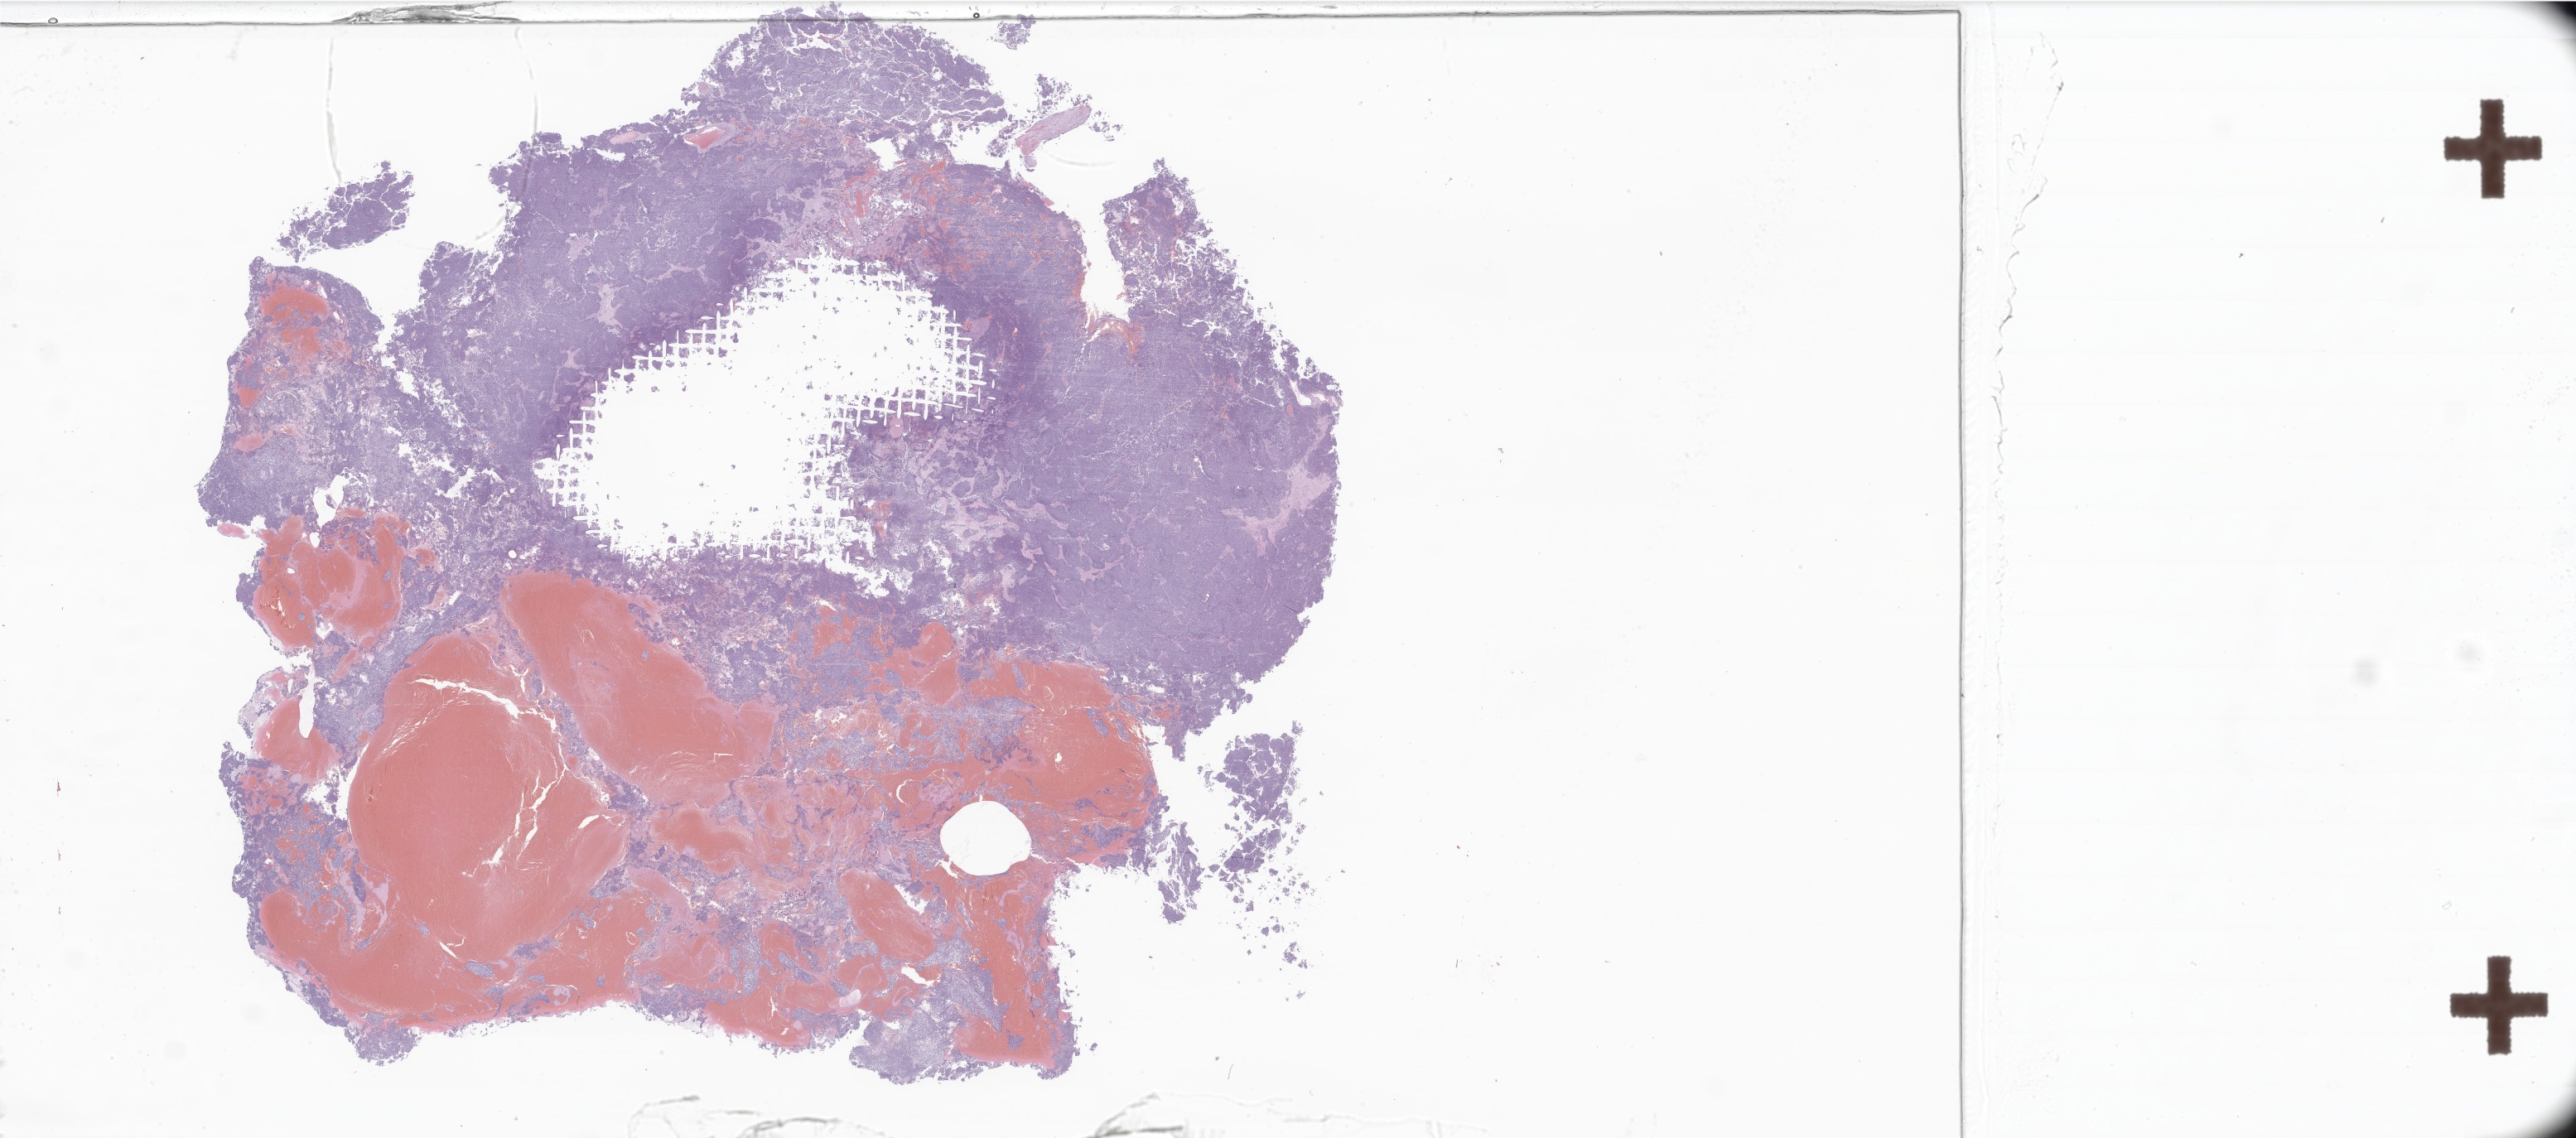
Digitized hematoxylin and eosin (H&E)-stained section of tumor tissue from the brain, a low-resolution overview of the entire scanned area, about 52.5 x 23.2 mm. FFPE section. Patient: male, age 83 months.
Diagnosis (ICD-O-3 morphology term): Tumor cells, uncertain whether benign or malignant.